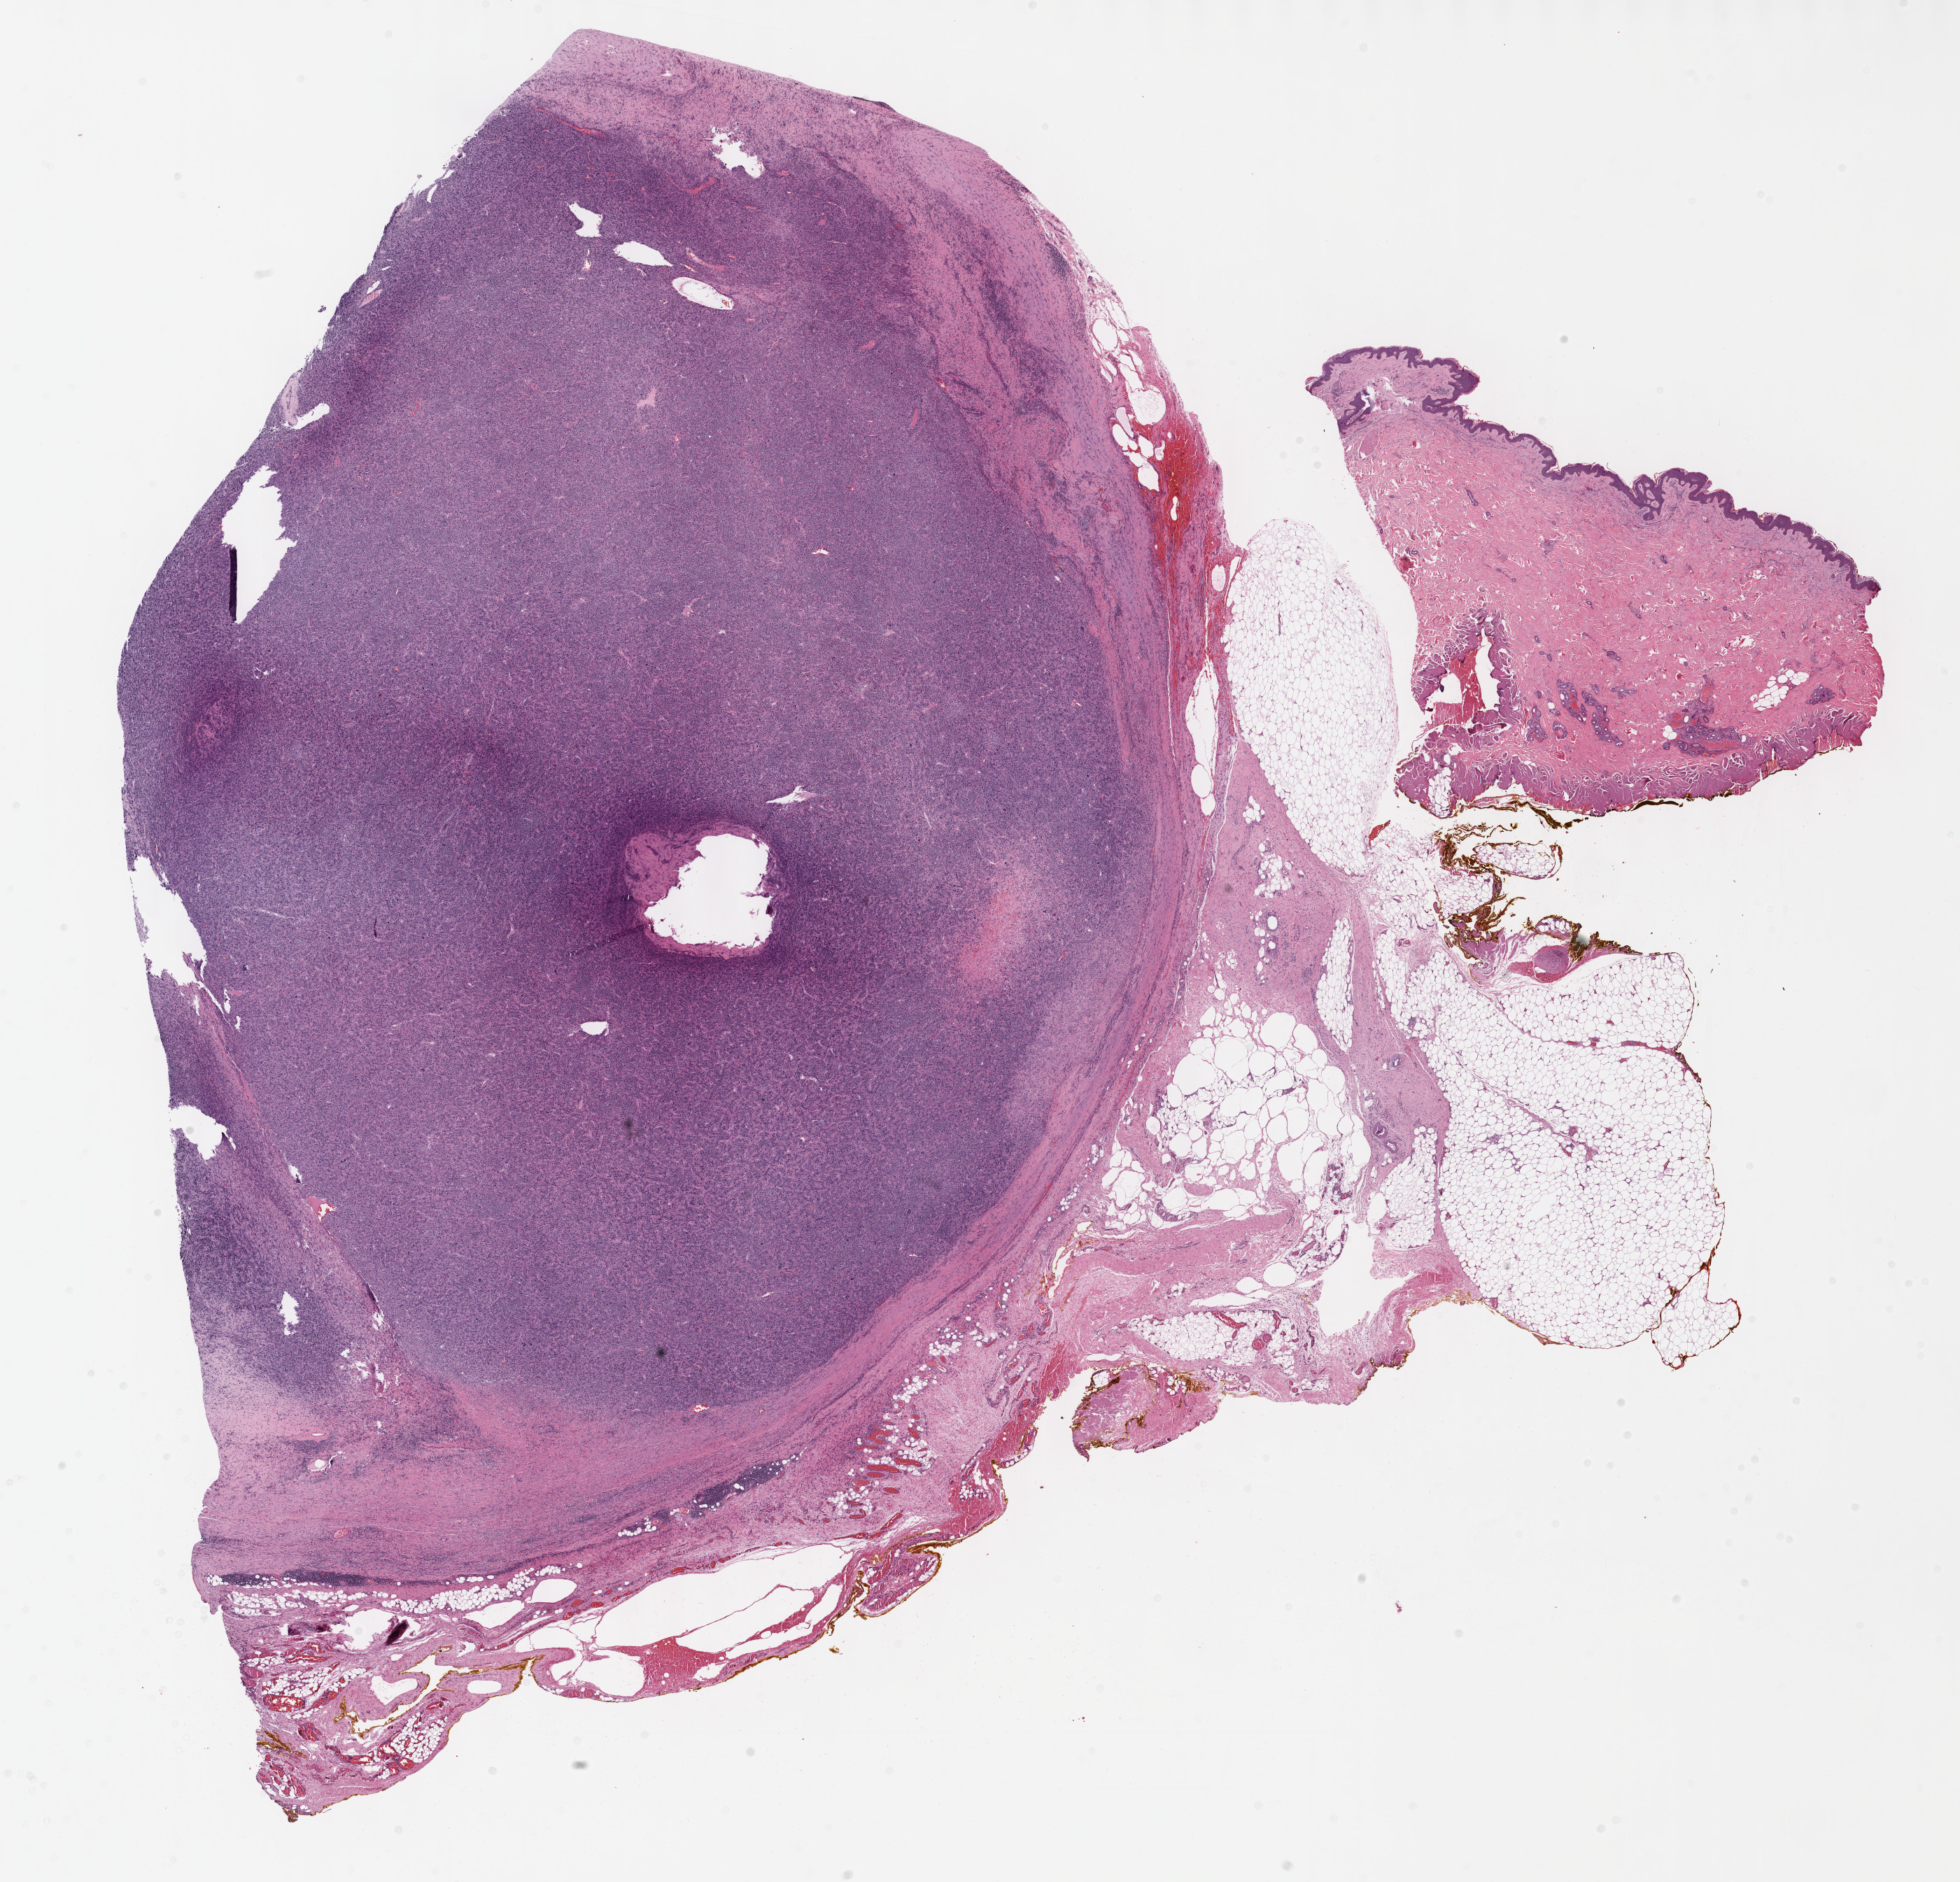
H&E-stained whole-slide image, shown as a low-resolution overview of the whole scanned area (about 22.6 x 21.7 mm, from a 40x scan), formalin-fixed paraffin-embedded (FFPE) diagnostic section, primary tumour sample from the connective, subcutaneous and other soft tissues. Male patient; age at initial diagnosis 71 years.
* histologic diagnosis: Undifferentiated sarcoma (connective, subcutaneous and other soft tissues of upper limb and shoulder)